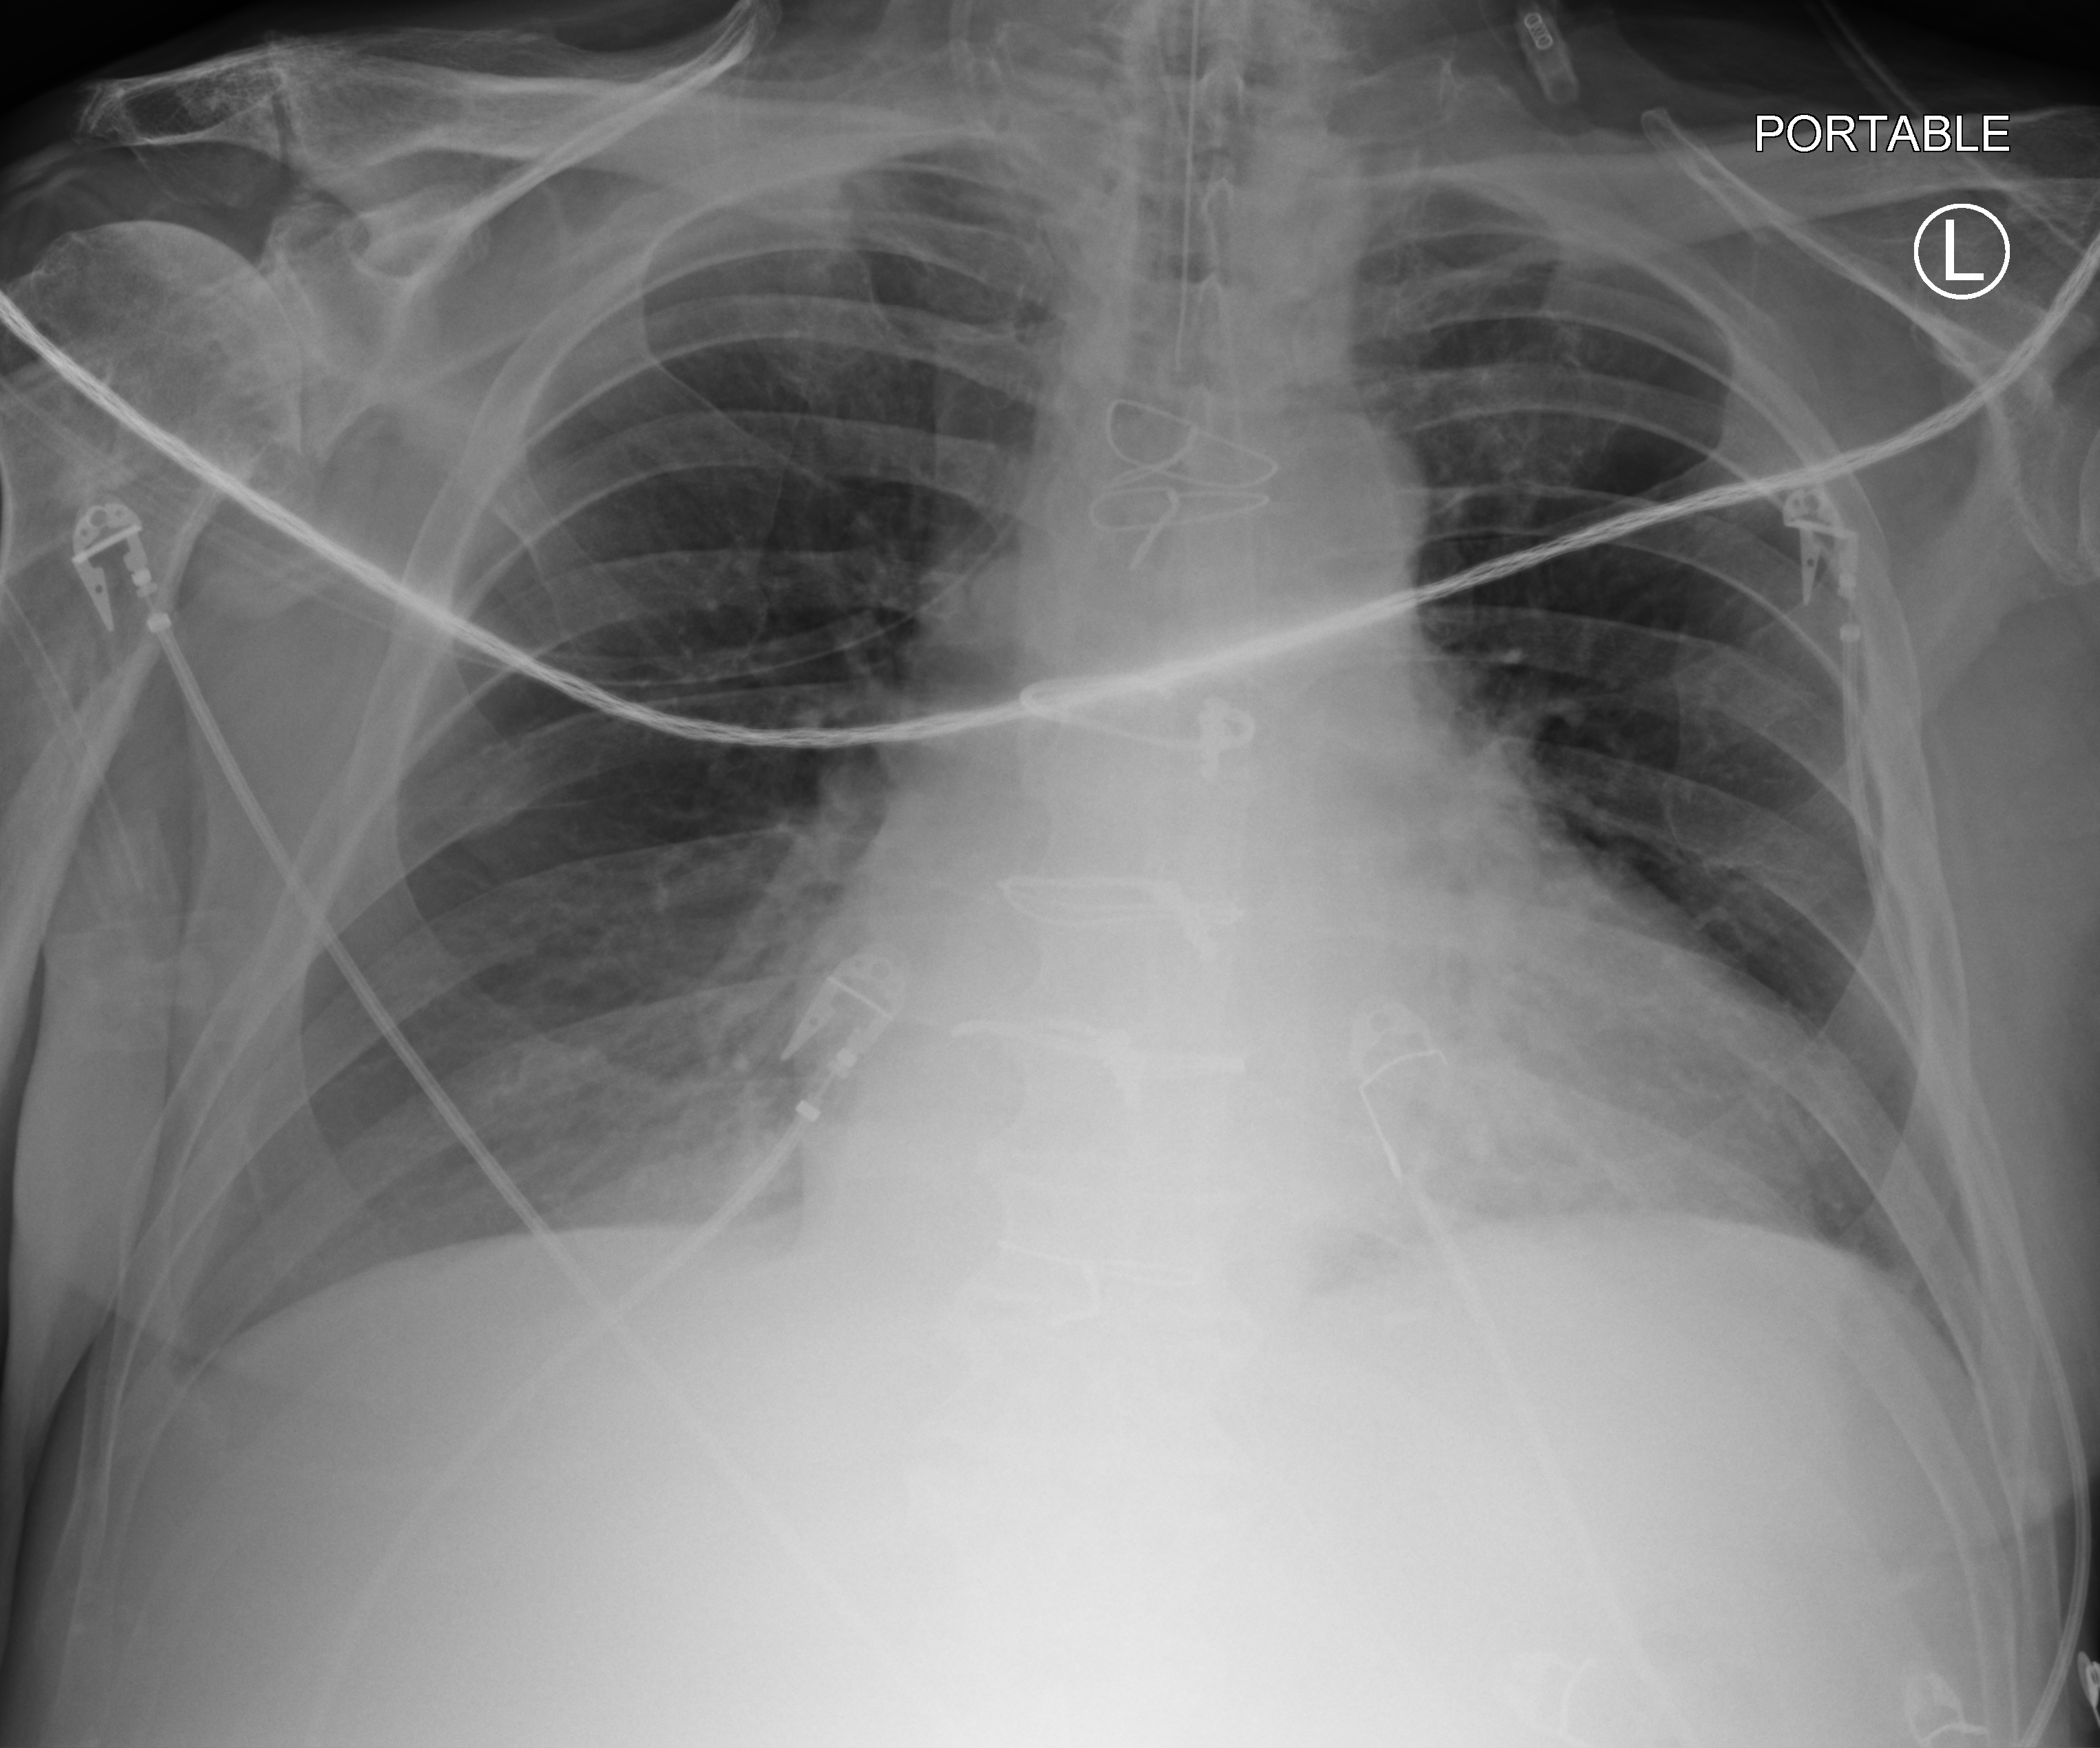
Portable chest radiograph, anteroposterior (AP) projection. Patient hospitalised with COVID-19; male, aged 60–74 years.
Admission-level facts for this patient (not findings on this image; timing relative to this image not recorded):
- length of hospital stay: 16 days
- mechanically ventilated during this hospital stay: yes
- chronic kidney disease (admission record): yes